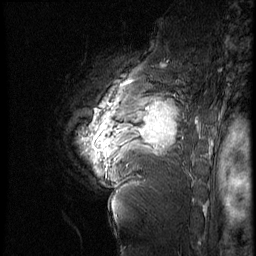
Breast MRI (dynamic contrast-enhanced), one sagittal slice; position 50 of 60 along the scan axis; 4 images stored at this slice position (order not interpretable as contrast timing); 1.5 T; TE 4.2 ms, TR 9 ms; 256 × 256 image matrix. Female patient, age 56 years. Case-level facts recorded for this patient, not image findings: setting: breast cancer imaged before/during neoadjuvant chemotherapy; receptor status: HER2-positive.
Annotated regions visible in this slice (semi-automatic segmentation, software-assisted and operator-edited):
- analysis volume of interest (the breast-tissue region the enhancement analysis was run in; not a lesion): bounding box [x1, y1, x2, y2] px = [82, 83, 199, 177]
- tumour enhancement mask (voxels above the 140 % enhancement threshold inside the analysis volume of interest): [94, 101, 179, 152]